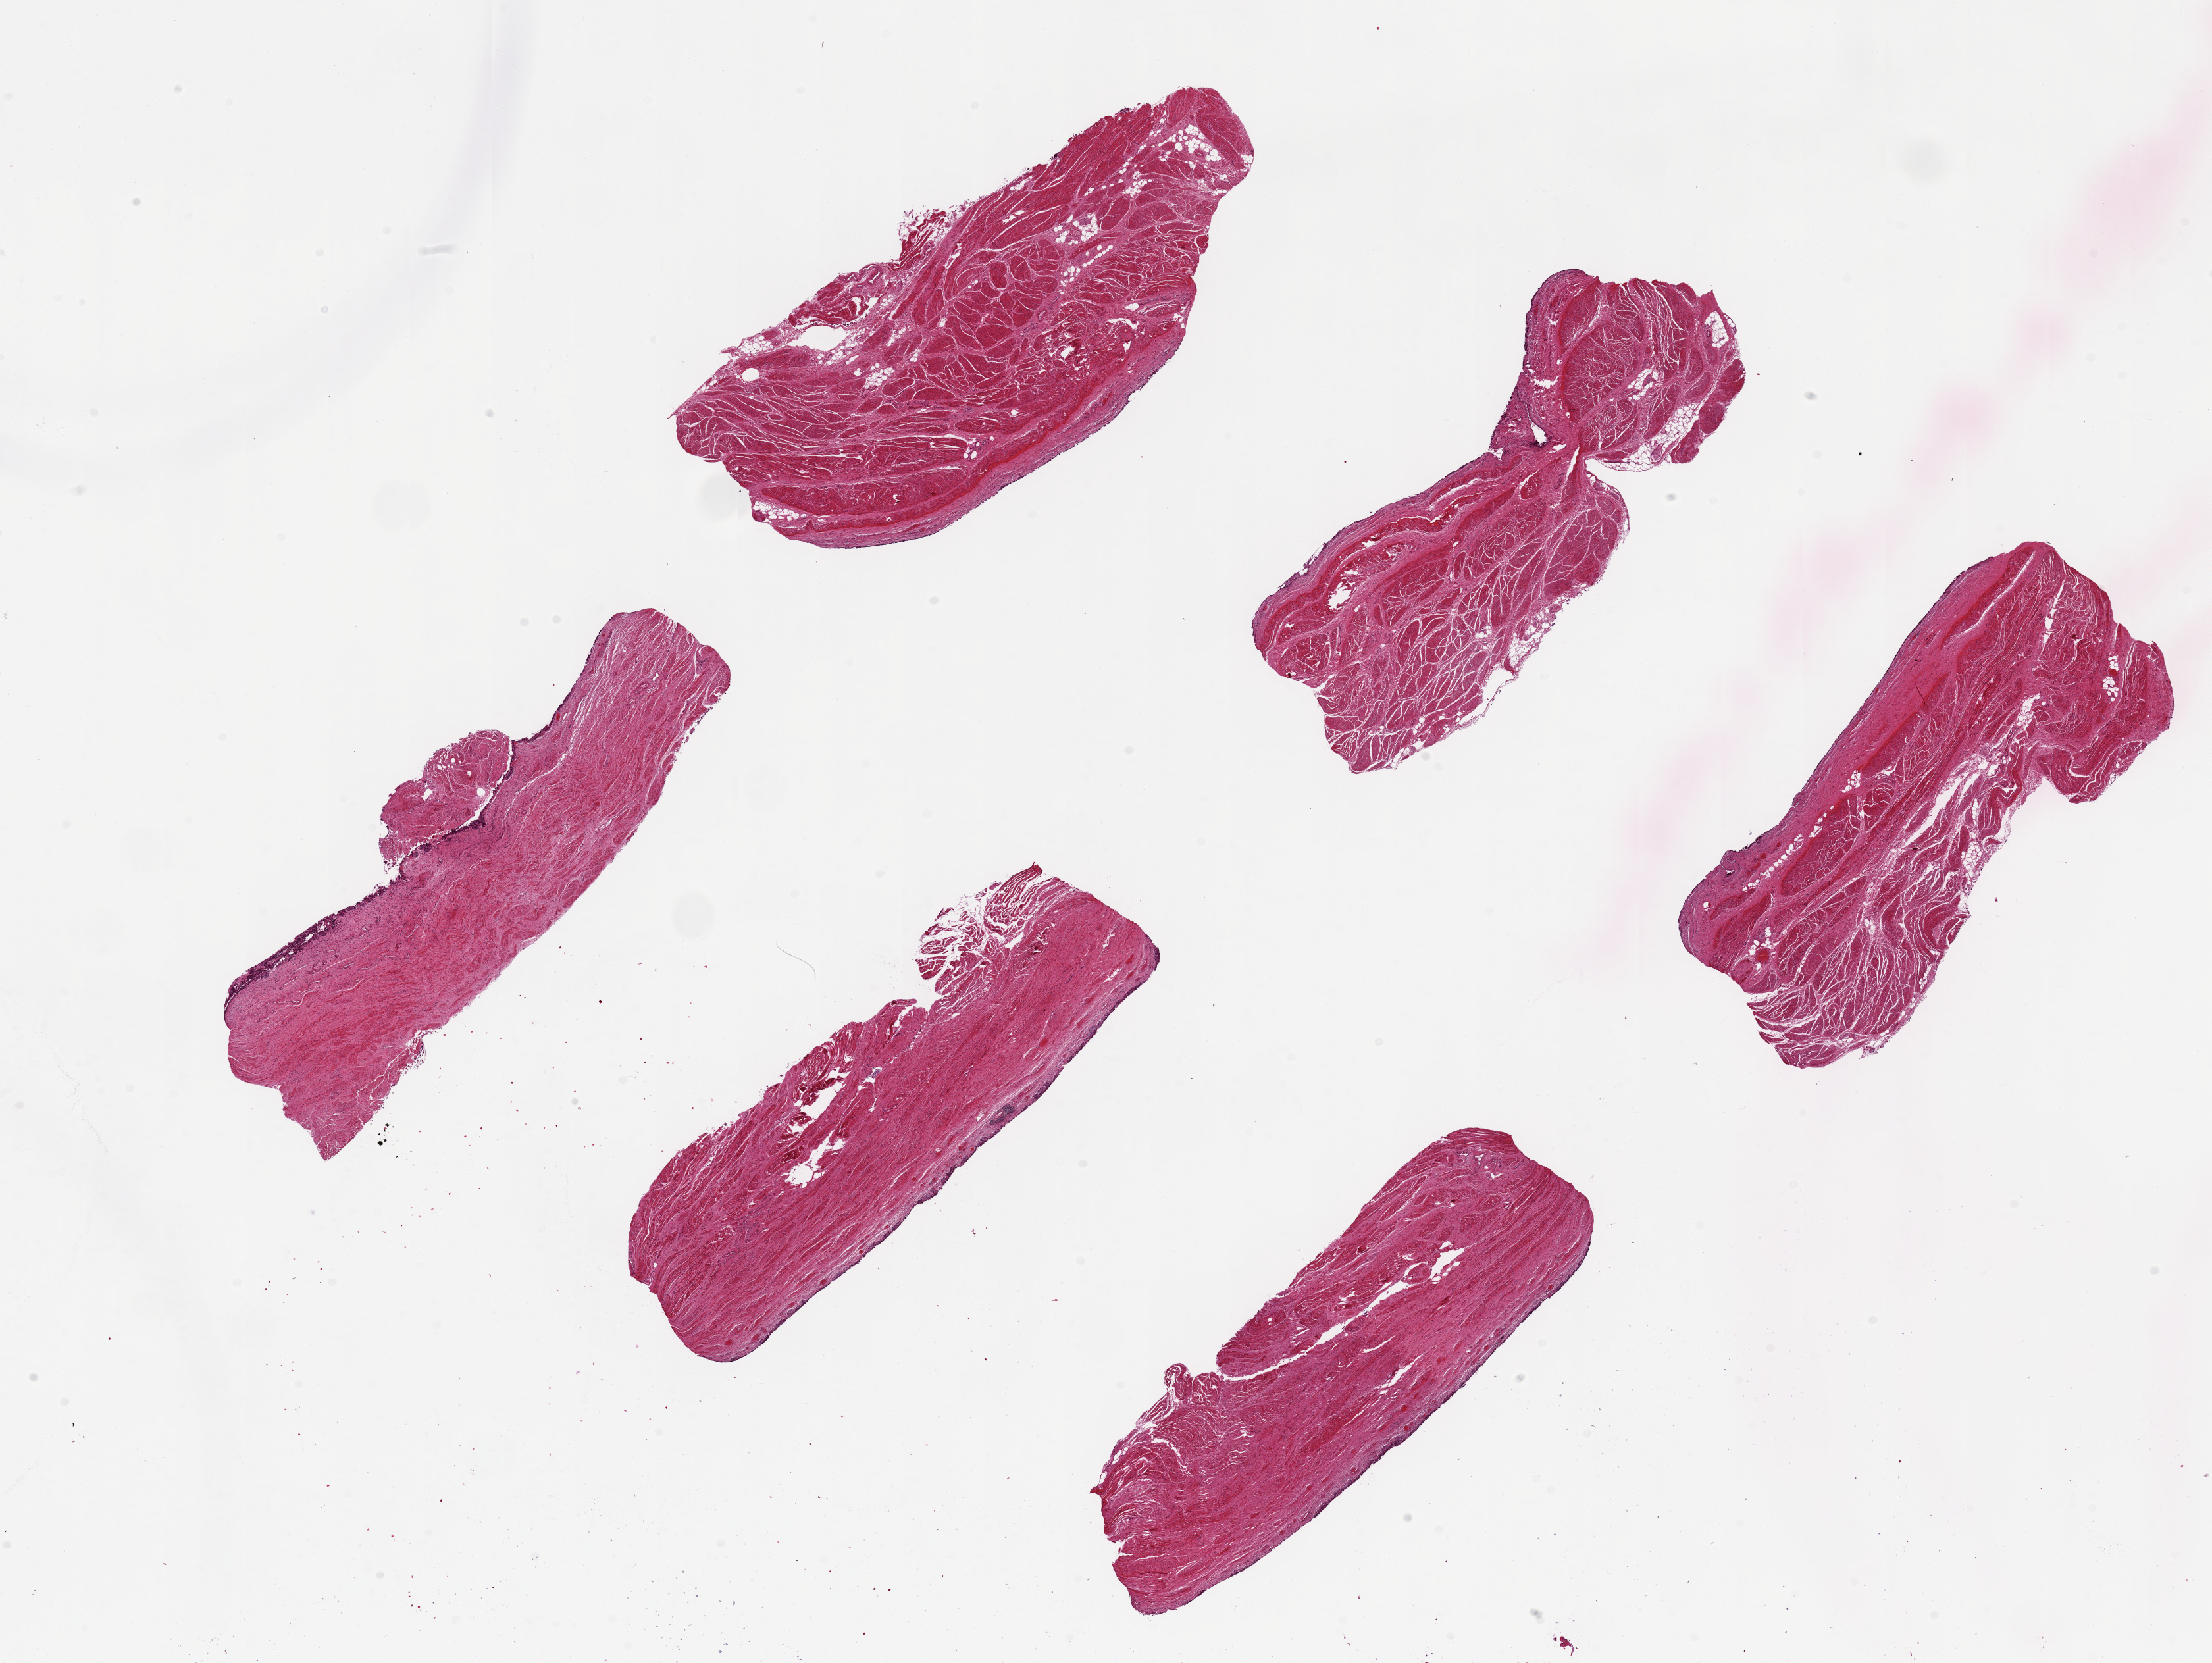
Haematoxylin and eosin whole-slide image — shown as a low-resolution overview of the whole scanned area (about 26.6 x 20.0 mm). PAXgene-fixed, paraffin-embedded tissue. Target tissue: urinary bladder. Donor tissue sample. Male donor.
Reviewer comment on this tissue sample: 6 pieces ~7x2mm. Urothelium largely sloughed, where evaluable is 1-2% of thickness.